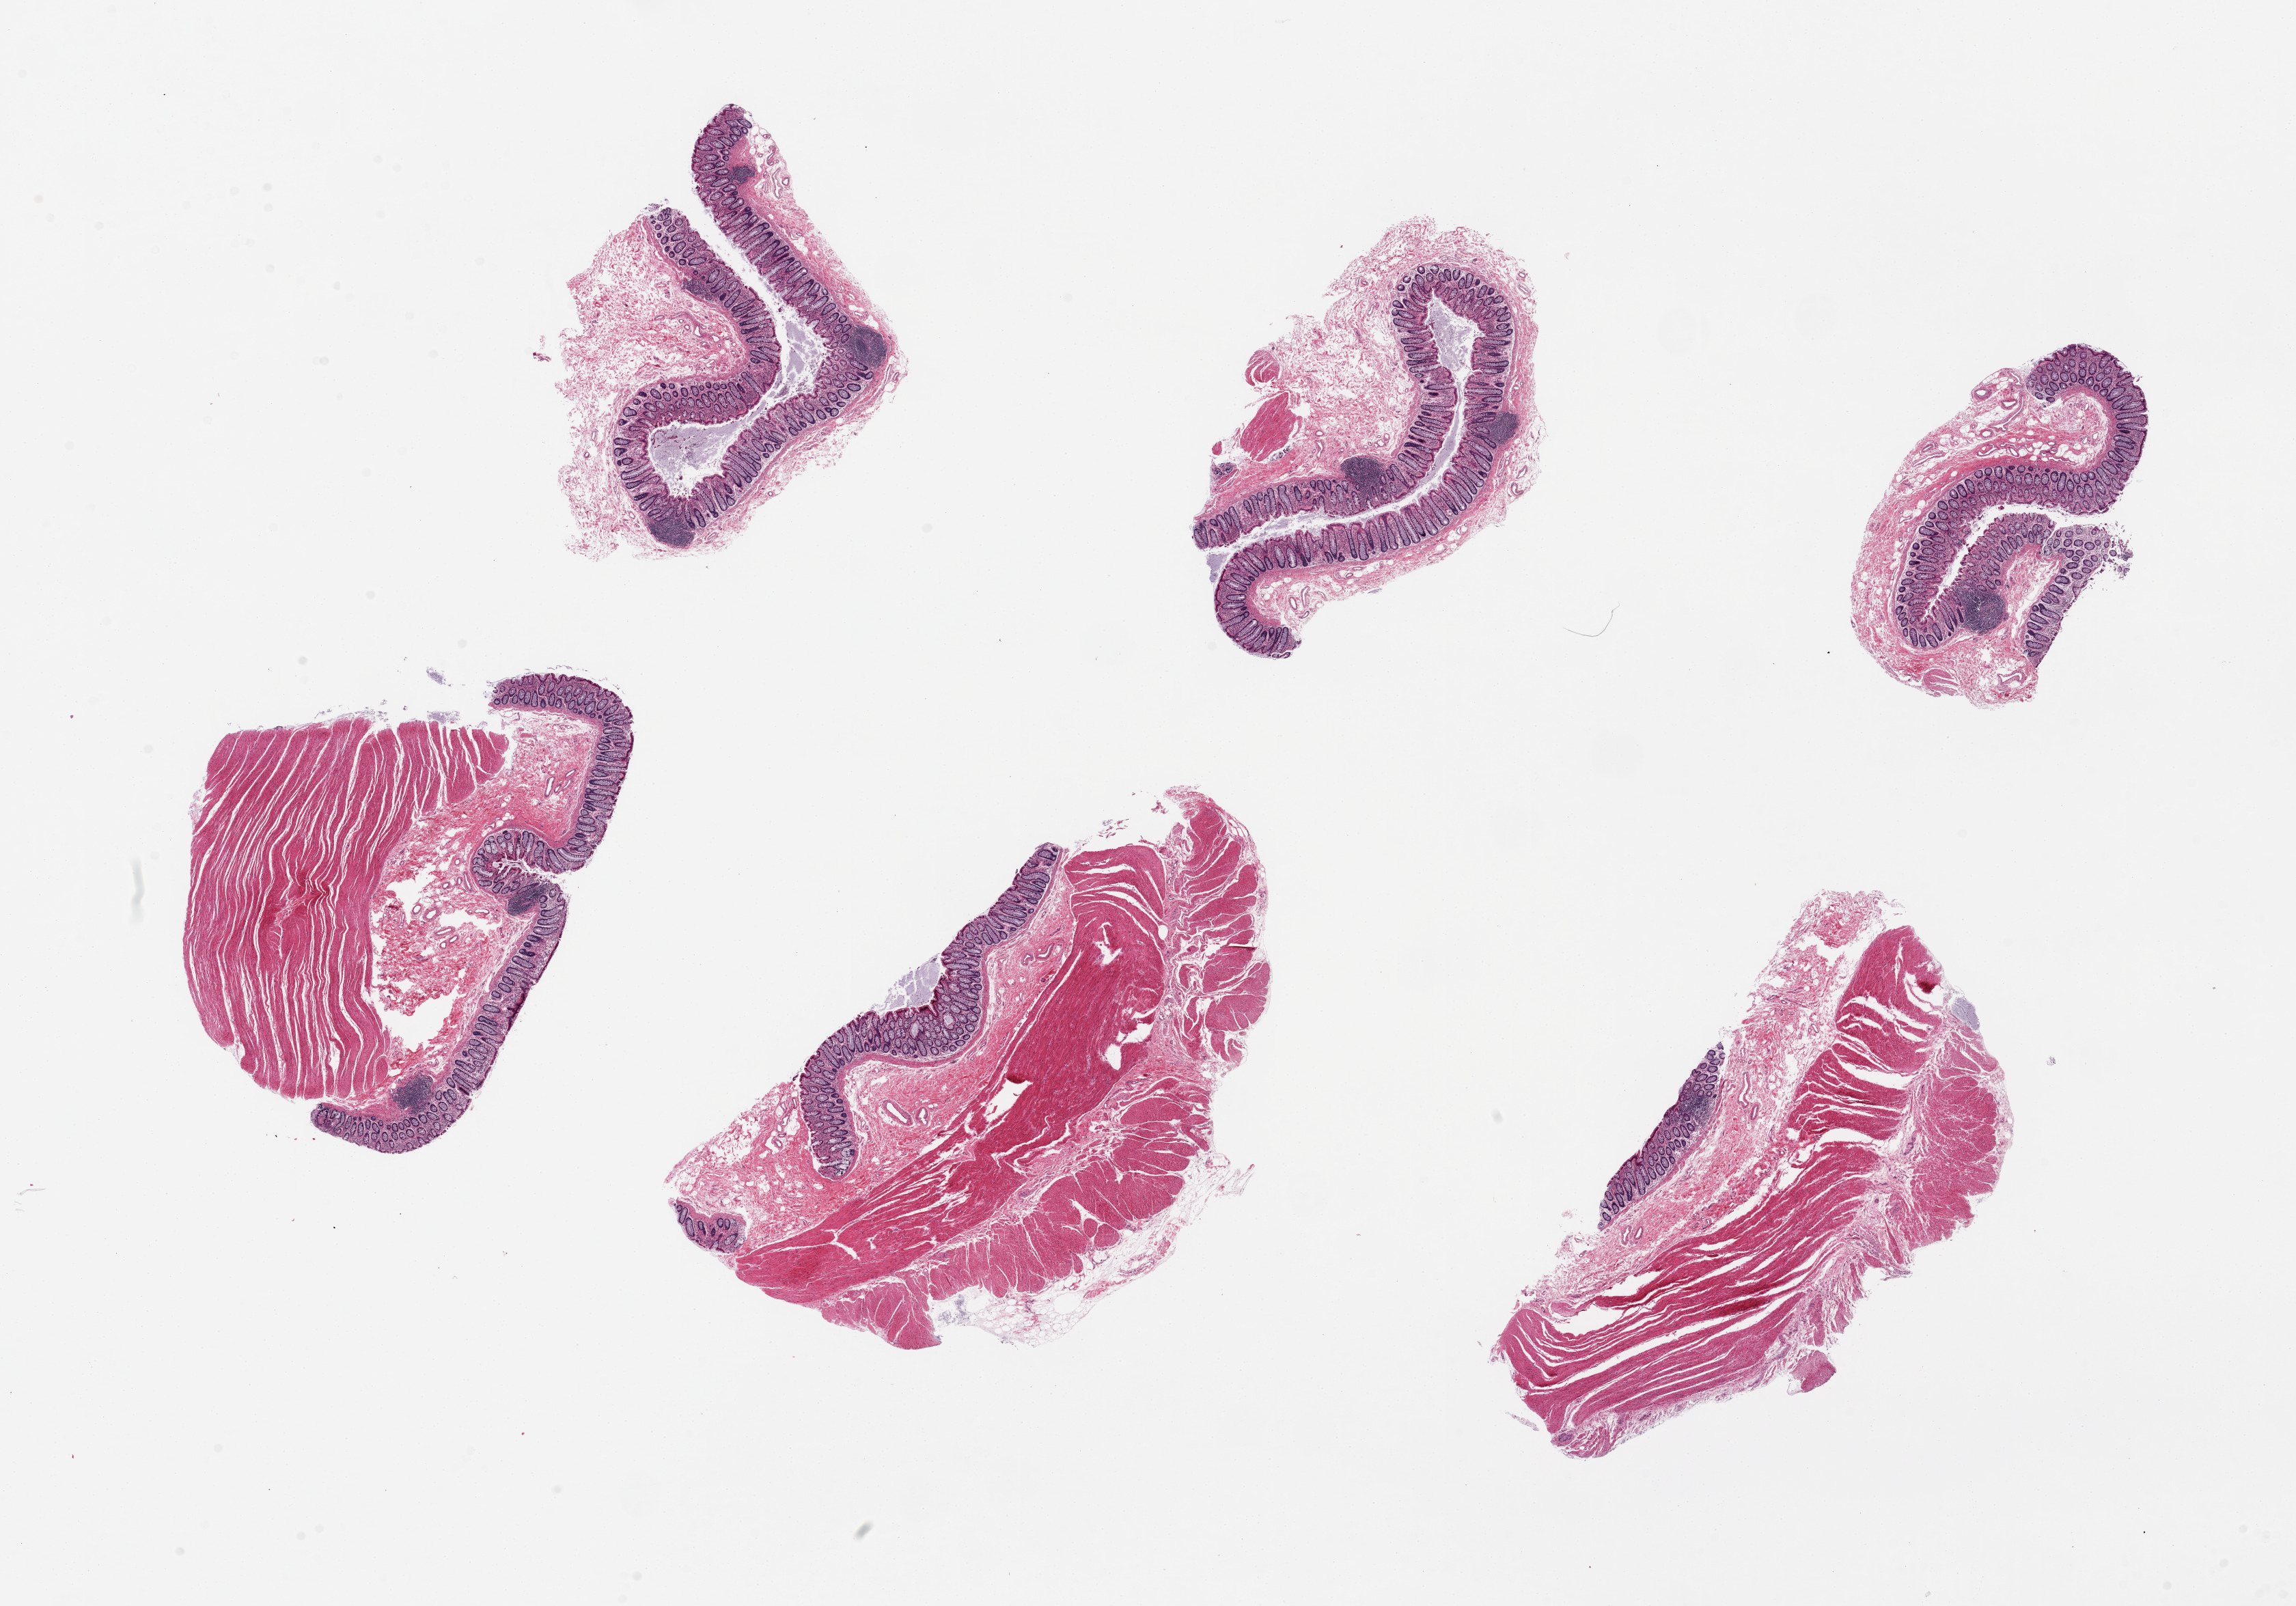
Haematoxylin and eosin whole-slide image, brightfield — low-resolution overview of the scanned area, about 26.6 x 18.6 mm, PAXgene-fixed, paraffin-embedded tissue, section of sigmoid colon (target tissue), tissue donor sample. Donor: male.
Pathologist's review note for this sample: 6 pieces, up to 8x5mm; 3 of 6 have mucosa only; 3 of 6 have mucosa and muscularis.